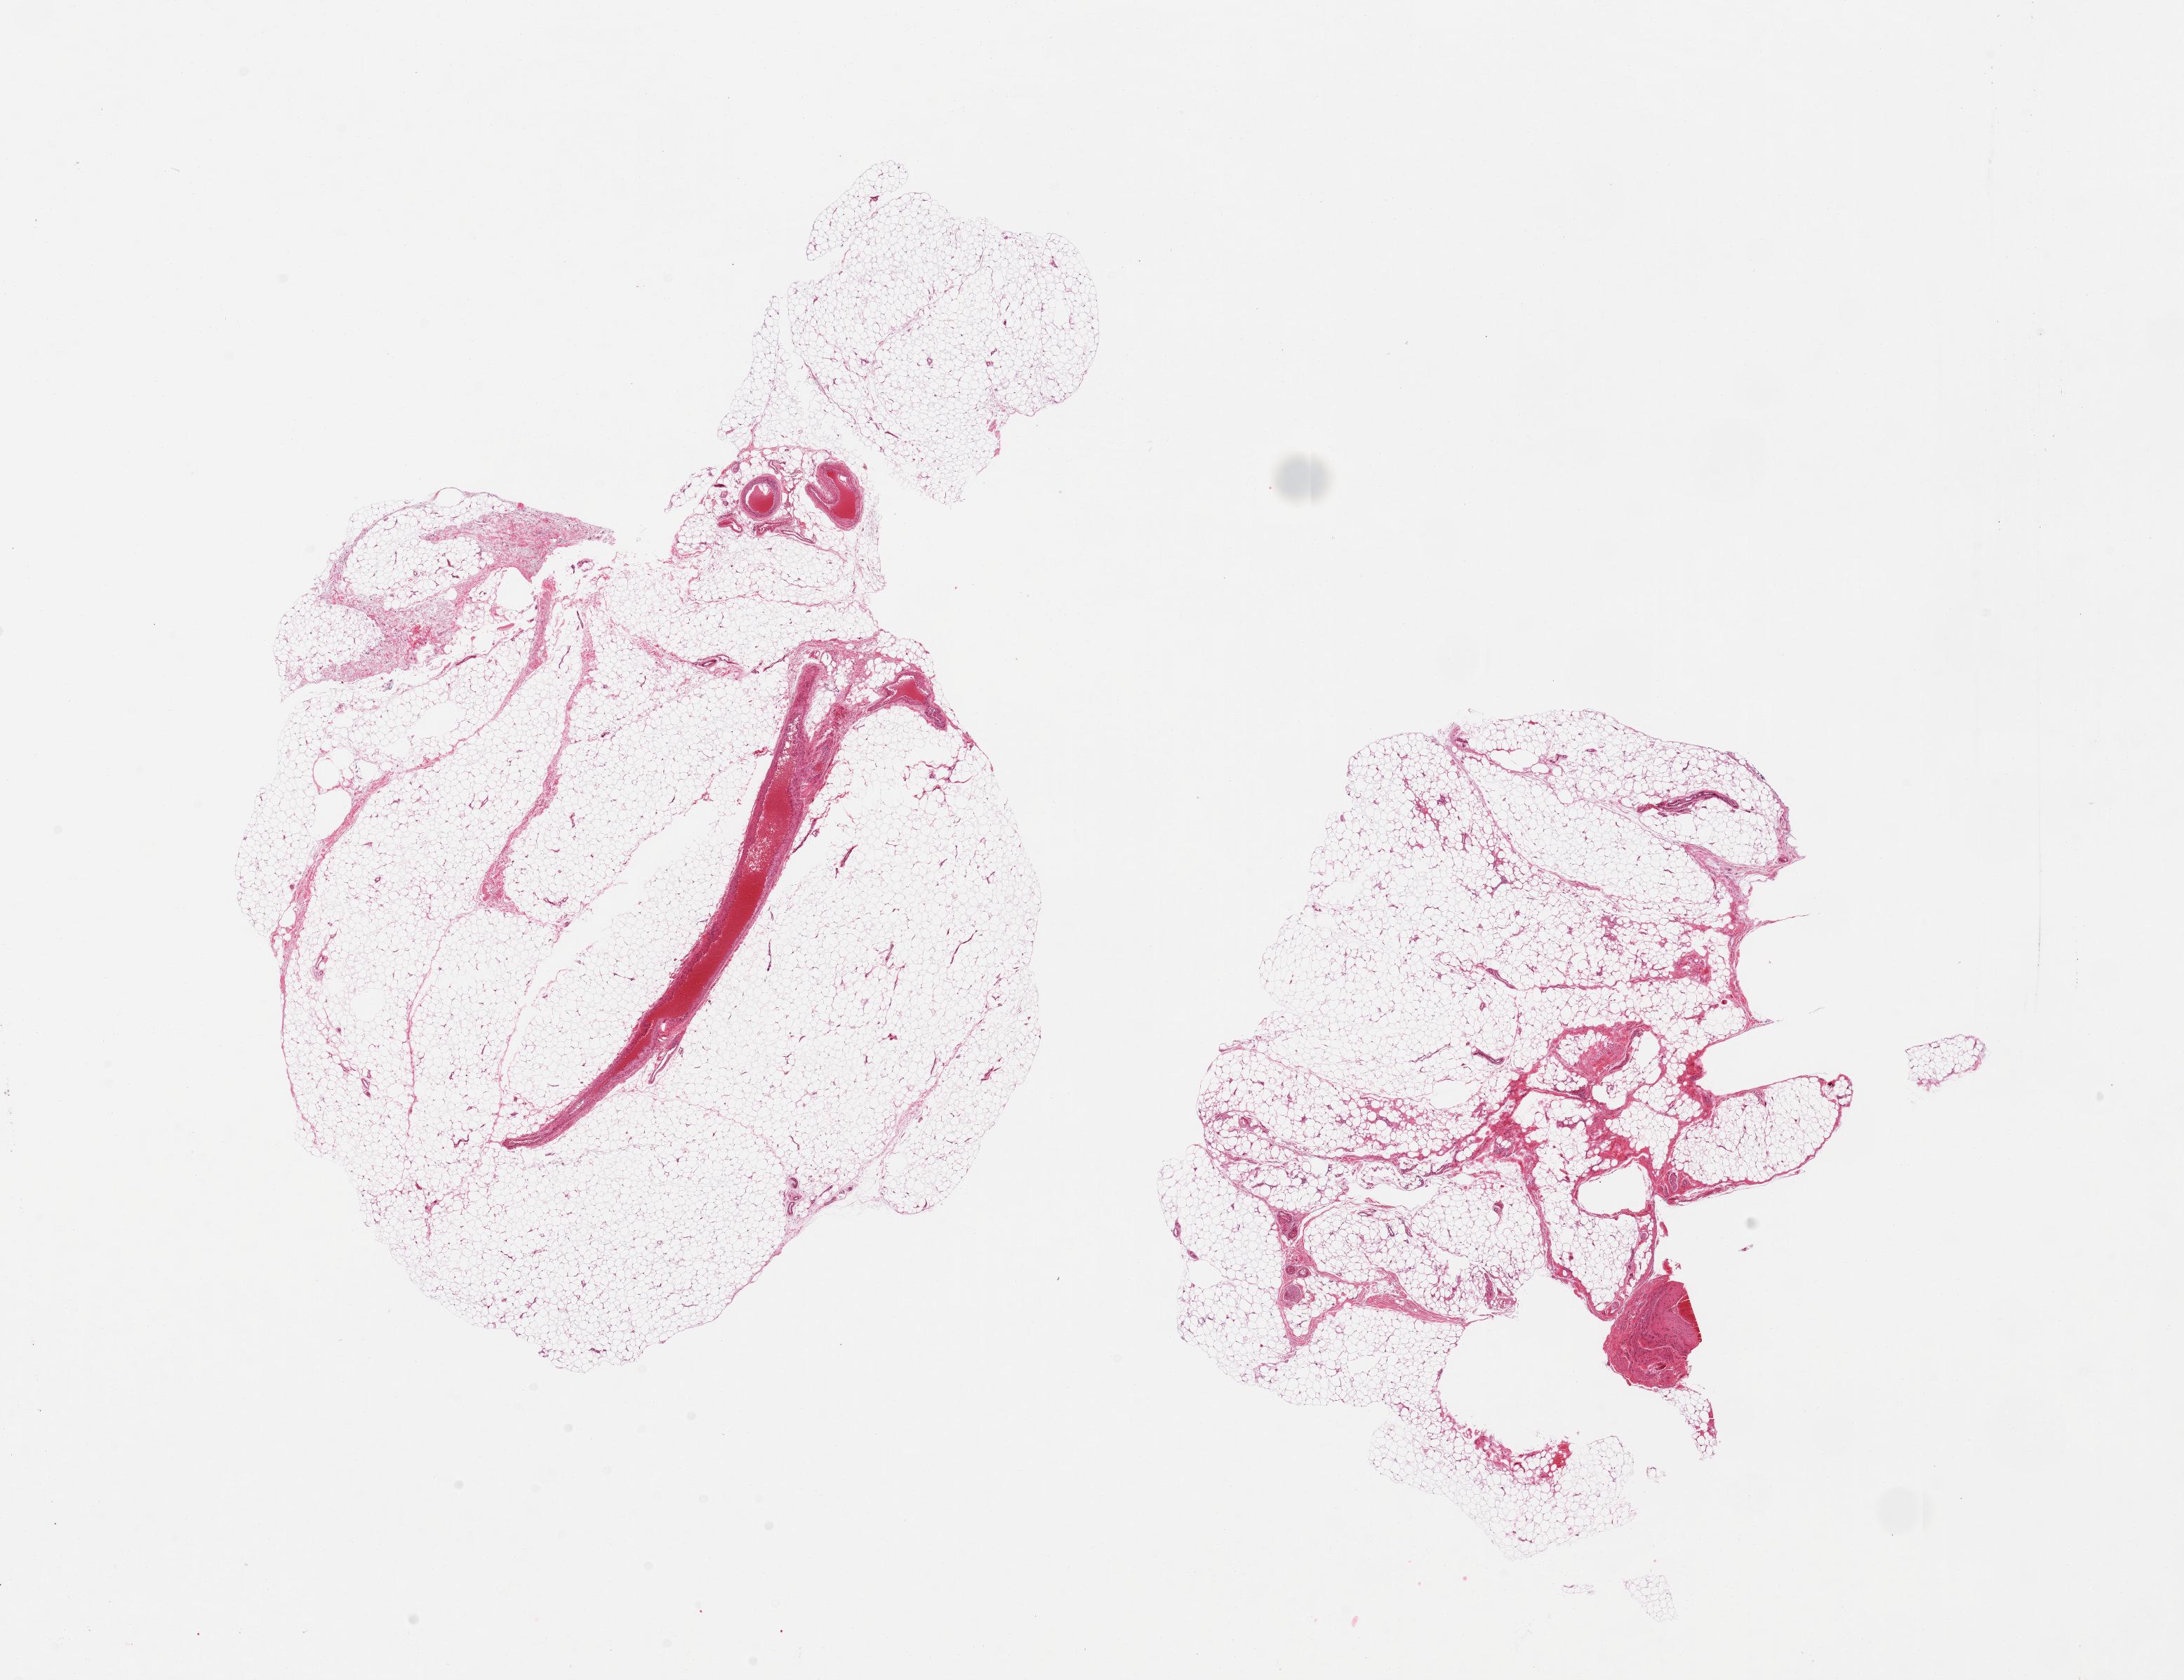
Digitized H&E-stained section, a low-resolution overview of the entire scanned area, about 24.6 x 18.9 mm. PAXgene-fixed paraffin-embedded (PFPE) section. Section of adipose tissue (target tissue). Tissue donor sample. Male donor.
• review note (as recorded): 2 pieces